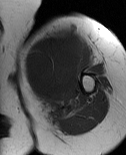
MRI of an extremity soft-tissue mass, one axial slice. Slice 54 of 86 in the series (ordered by position). MR volume resampled by the dataset authors to the PET/CT grid (not the native acquisition matrix). 3.27 mm slice thickness. 126 × 155 image matrix, field of view 123 × 151 mm. Female patient. Case-level facts recorded for this patient, not image findings: histological type: pleiomorphic leiomyosarcoma; grade: high; site of the primary tumour: left biceps.
Outlined on this slice (expert contour drawn on MRI and transferred to this co-registered scan by the dataset authors):
- gross tumour volume including surrounding oedema: bounding box <24,28,87,116> (left, top, right, bottom; pixels)
- gross tumour volume (mass): <24,29,83,102>